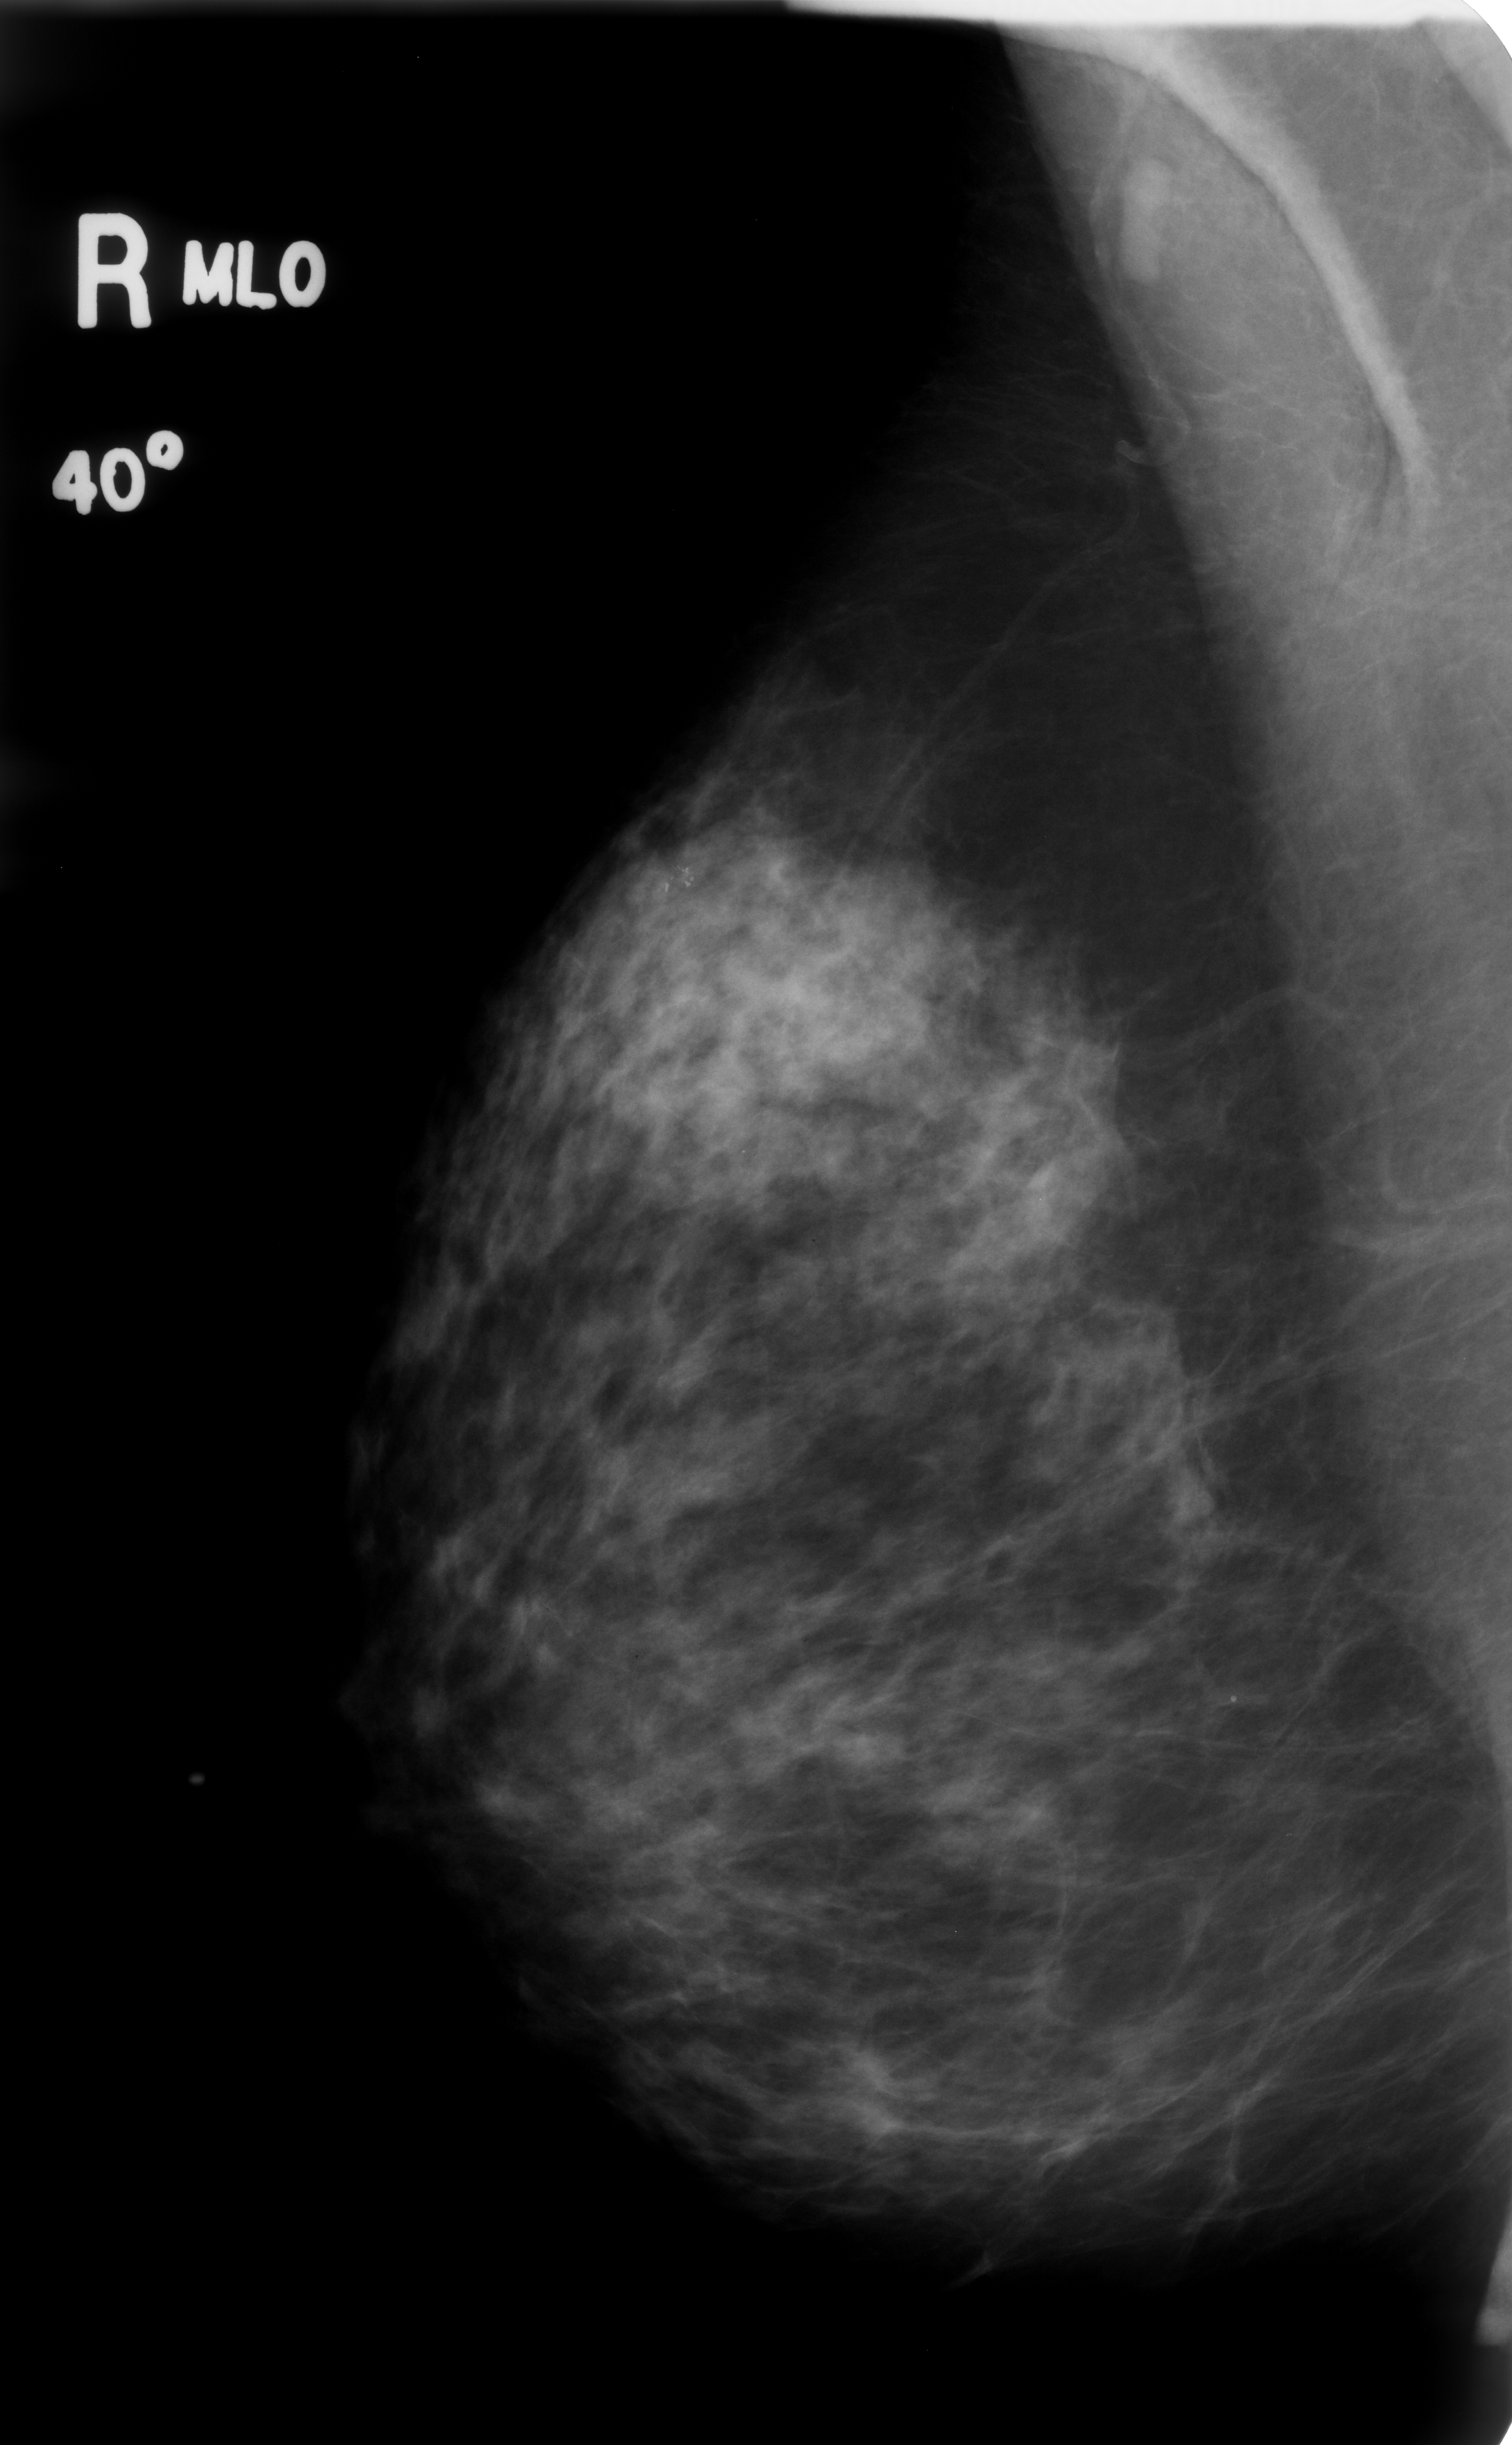
Mammogram (digitized film); right breast; mediolateral oblique (MLO) view; BI-RADS breast density category 3 (scale 1–4); 1512 × 2445 image matrix.
Expert-marked regions of interest on this film, with their recorded descriptors:
- calcifications, morphology pleomorphic, distribution clustered; BI-RADS assessment category 4; subtlety rating 4 on a 1 (subtle) to 5 (obvious) scale; pathology result (as recorded, not read from the image): benign: bounding box (x1, y1, x2, y2) in pixels: (617, 819, 723, 950)